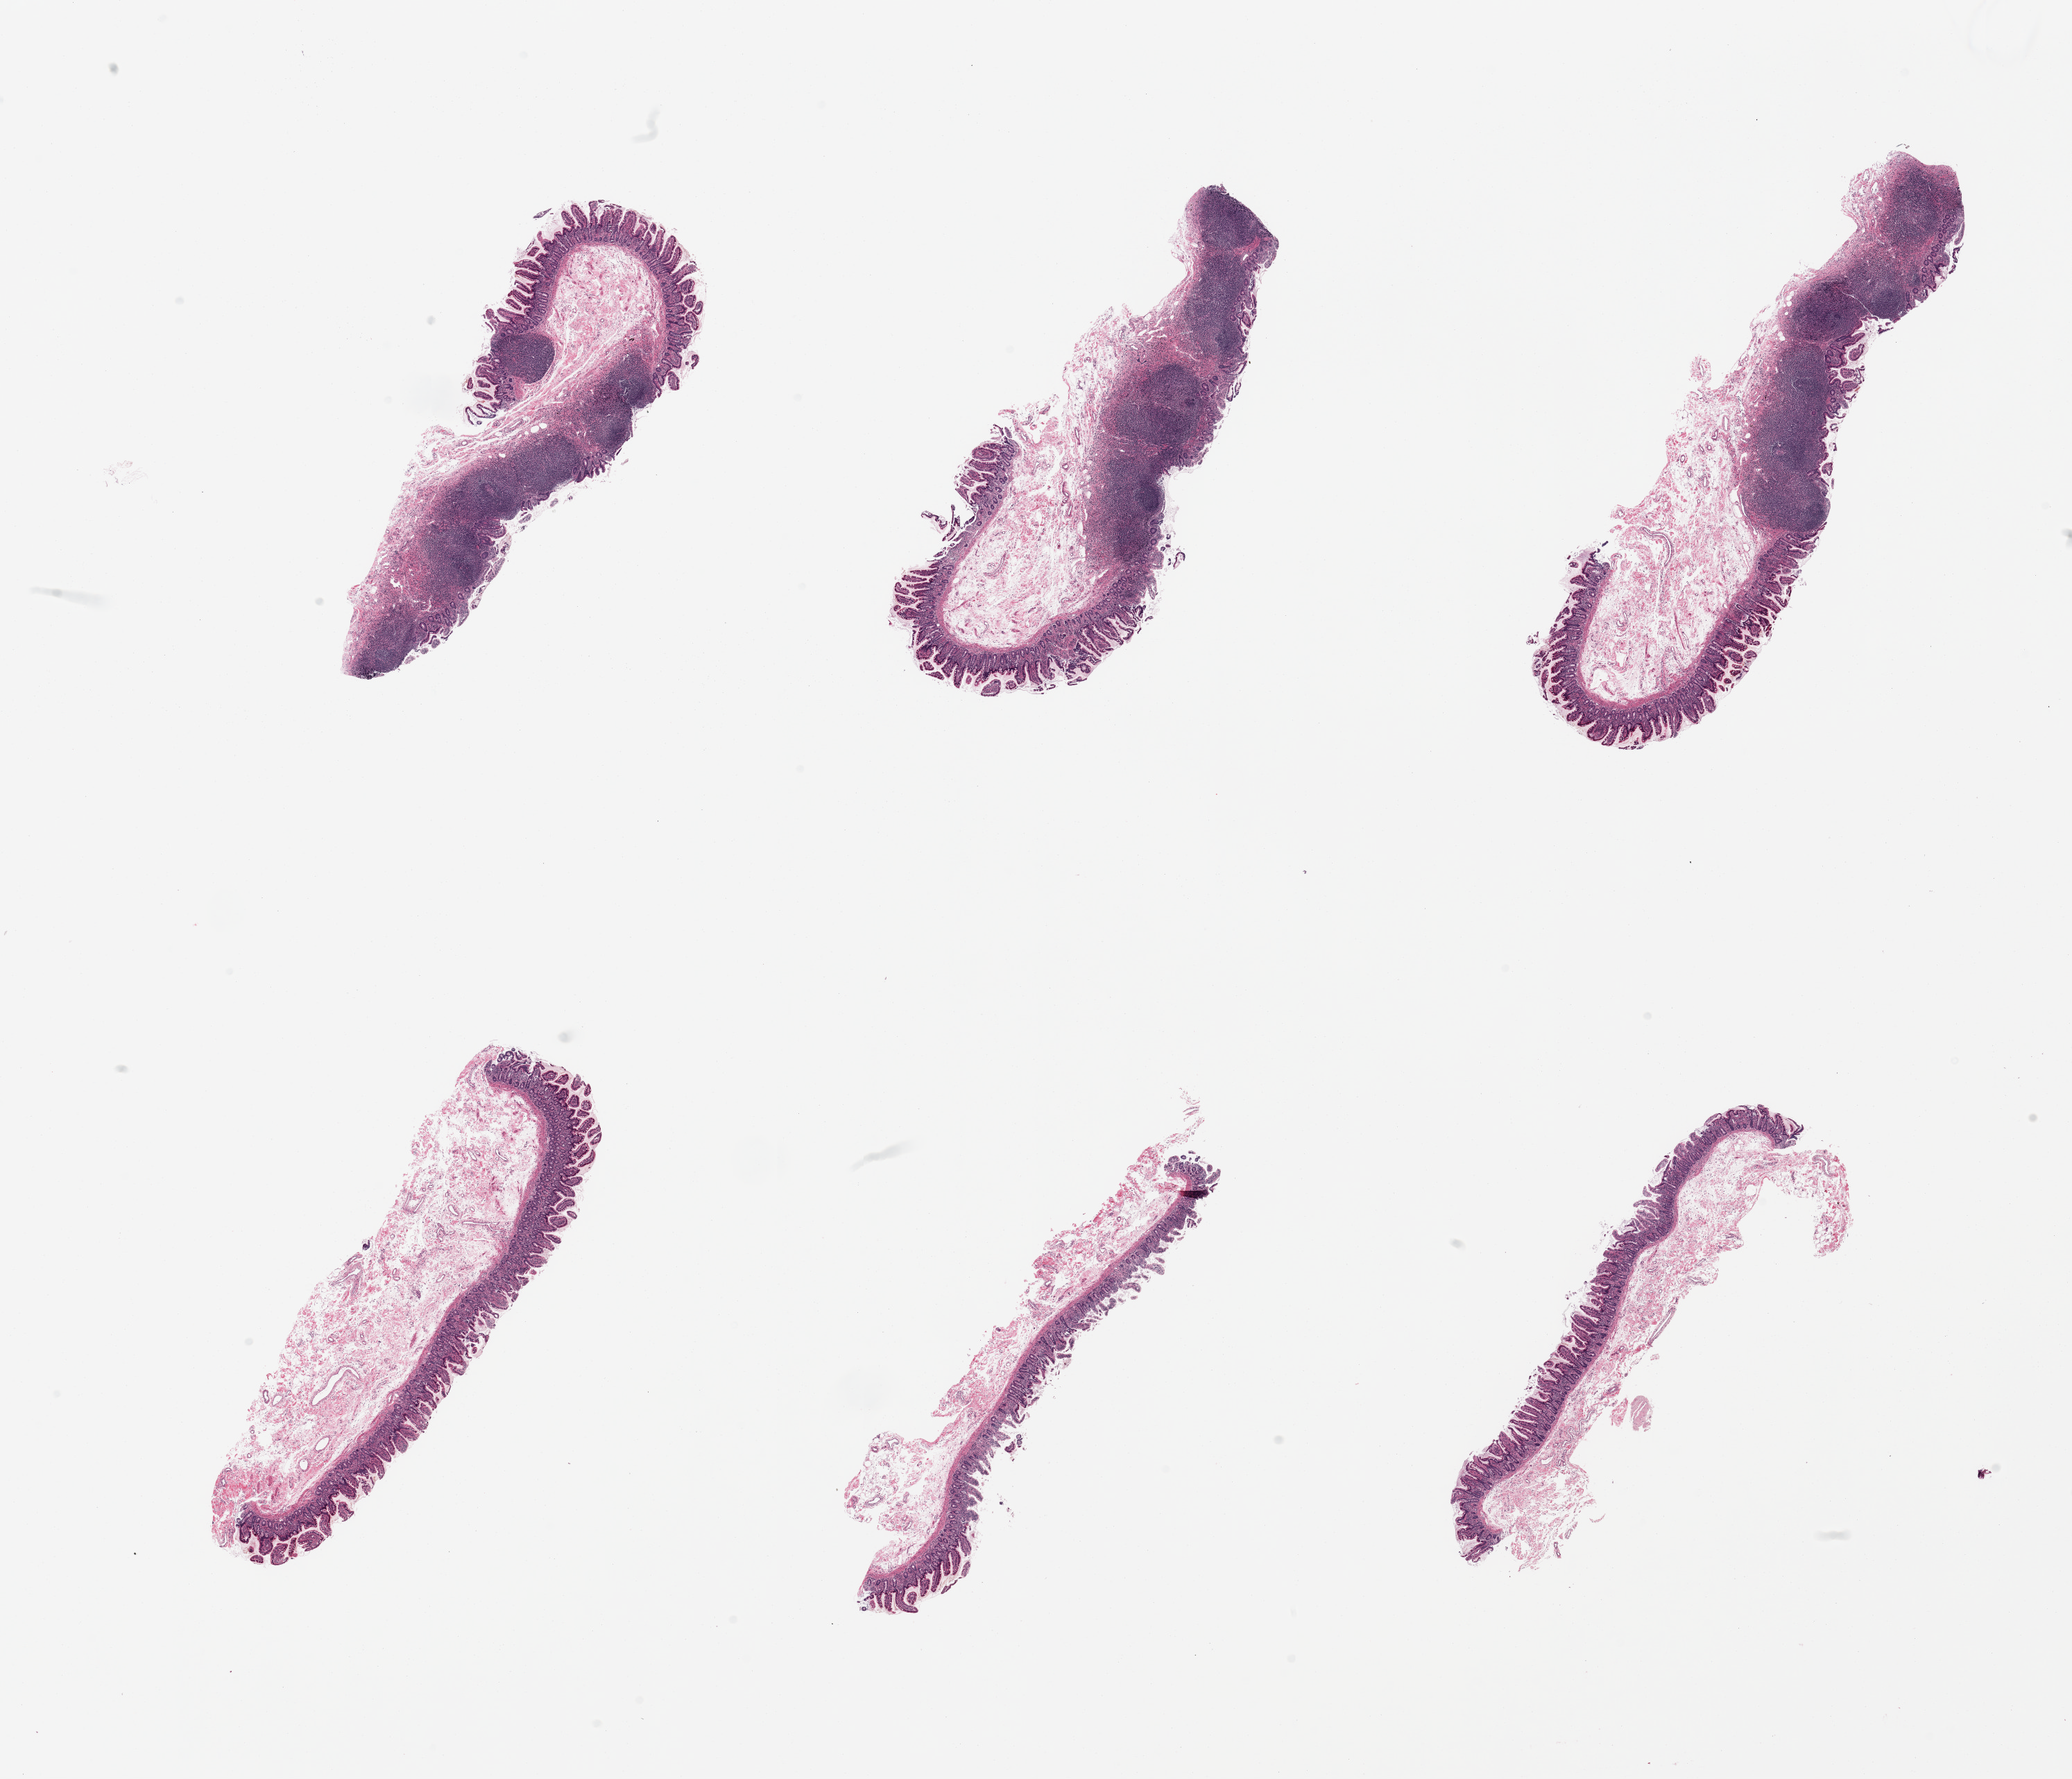
Haematoxylin and eosin whole-slide image, shown as a low-resolution overview of the whole scanned area (about 23.6 x 20.3 mm, acquisition: 20x scan). PAXgene-fixed, paraffin-embedded tissue. Section of ileum (target tissue). Tissue donor sample. Male donor.
Pathologist's review note for this sample: 6 pieces; mucosa and submucosa with good lymphoid tissue in 3 of 6.